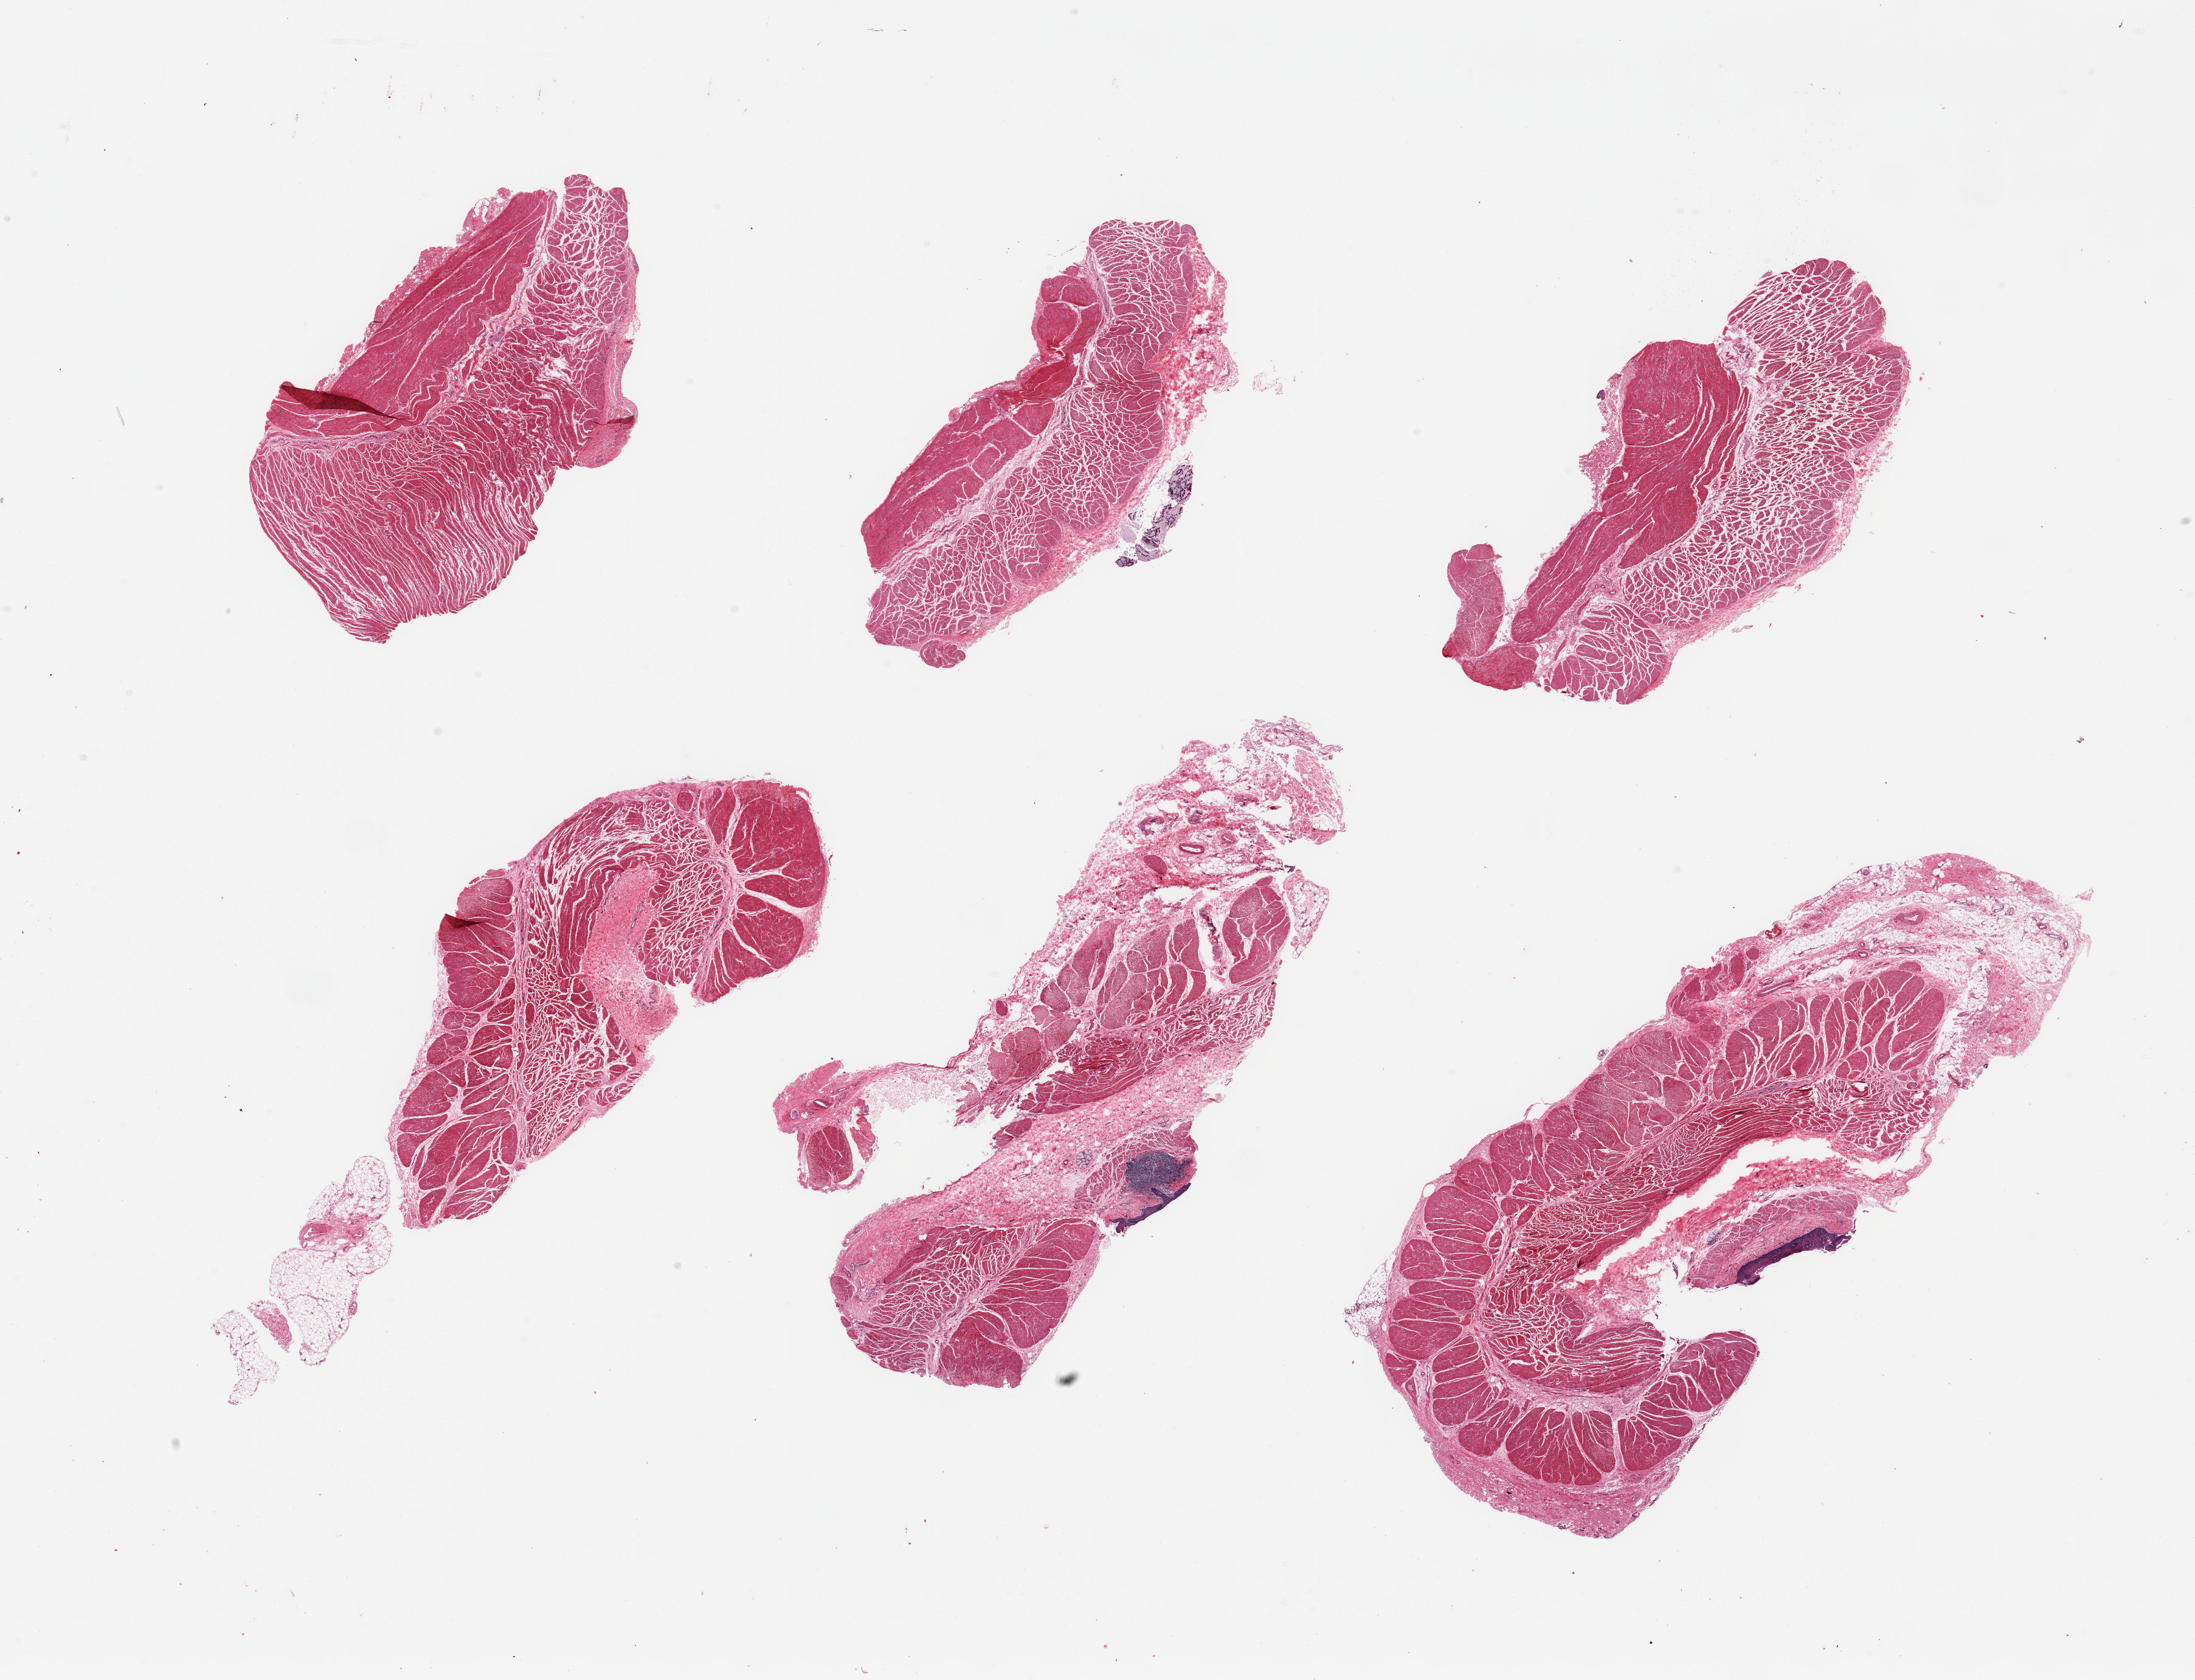
Whole-slide image, hematoxylin and eosin (H&E) stain — low-resolution overview of the scanned area, about 28.5 x 21.9 mm (from a 20x scan); PAXgene-fixed, paraffin-embedded tissue; section of esophageal muscle (target tissue); donor tissue sample.
* reviewer comment on this tissue sample: 6 pieces; foci of squamous epithelium and glandular carry-over <5% area